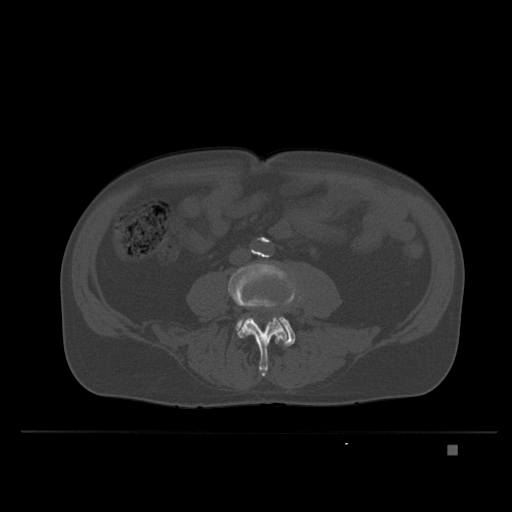
CT including the spine, one axial slice; slice 70 of 435 in the series (ordered by position); bone window (W 1800 / L 400 HU); 1.5 mm slice thickness; 512 × 512 image matrix, field of view 434 × 434 mm. Male patient, age 73 years. Case-level facts recorded for this patient, not image findings: primary cancer: skin.
Structures marked on this image (semi-automatically segmented with operator editing):
- L4 vertebra: bounding box <228,261,299,377> (left, top, right, bottom; pixels)
- L5 vertebra: <236,297,301,347>